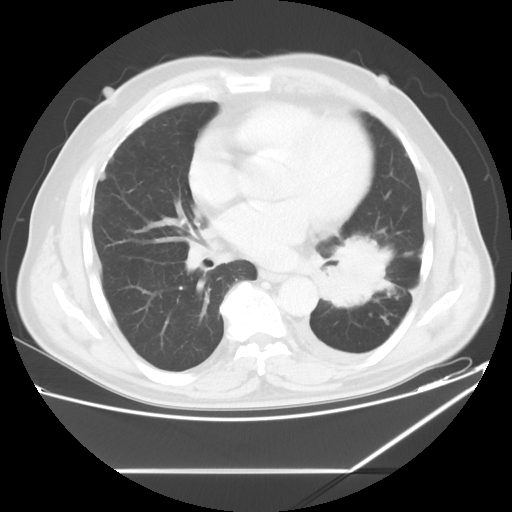
Chest CT, one axial slice; position 28 of 60 along the scan axis; 120 kVp; lung window (W 1500 / L -600 HU); 512 × 512 image matrix. Patient: male, 62 years. From the clinical record (not read from this slice): clinical TNM (as recorded): T3 N0 M1.
Annotated regions visible in this slice (rectangle marked by the reading radiologist):
- lung tumour (recorded histology: adenocarcinoma): bounding box (x1, y1, x2, y2) in pixels: (316, 233, 392, 313)
- lung tumour (recorded histology: adenocarcinoma): (321, 232, 391, 315)